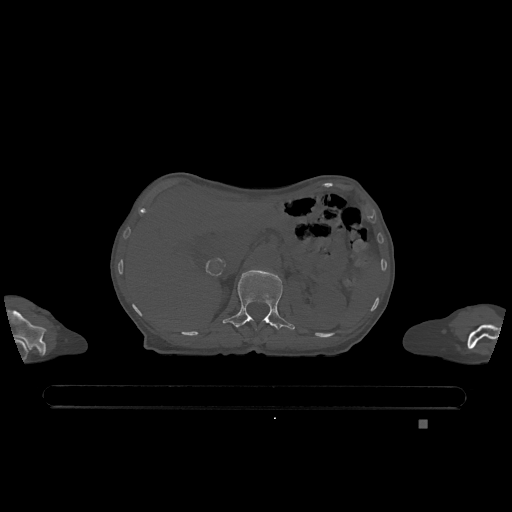
CT including the spine, one axial slice. Slice 479 of 1317 in the series (ordered by position). Bone window (W 1800 / L 400 HU). 0.5 mm slice thickness. 512 × 512 image matrix, field of view 500 × 500 mm. Patient: female, 74 years. From the clinical record (not read from this slice): primary cancer: lung; vertebrae with lytic lesions (as recorded): T1, T4, T5, T6, L4, L5.
Structures marked on this image (semi-automatically segmented with operator editing):
- L1 vertebra: box from (x=222, y=269) to (x=295, y=330) px